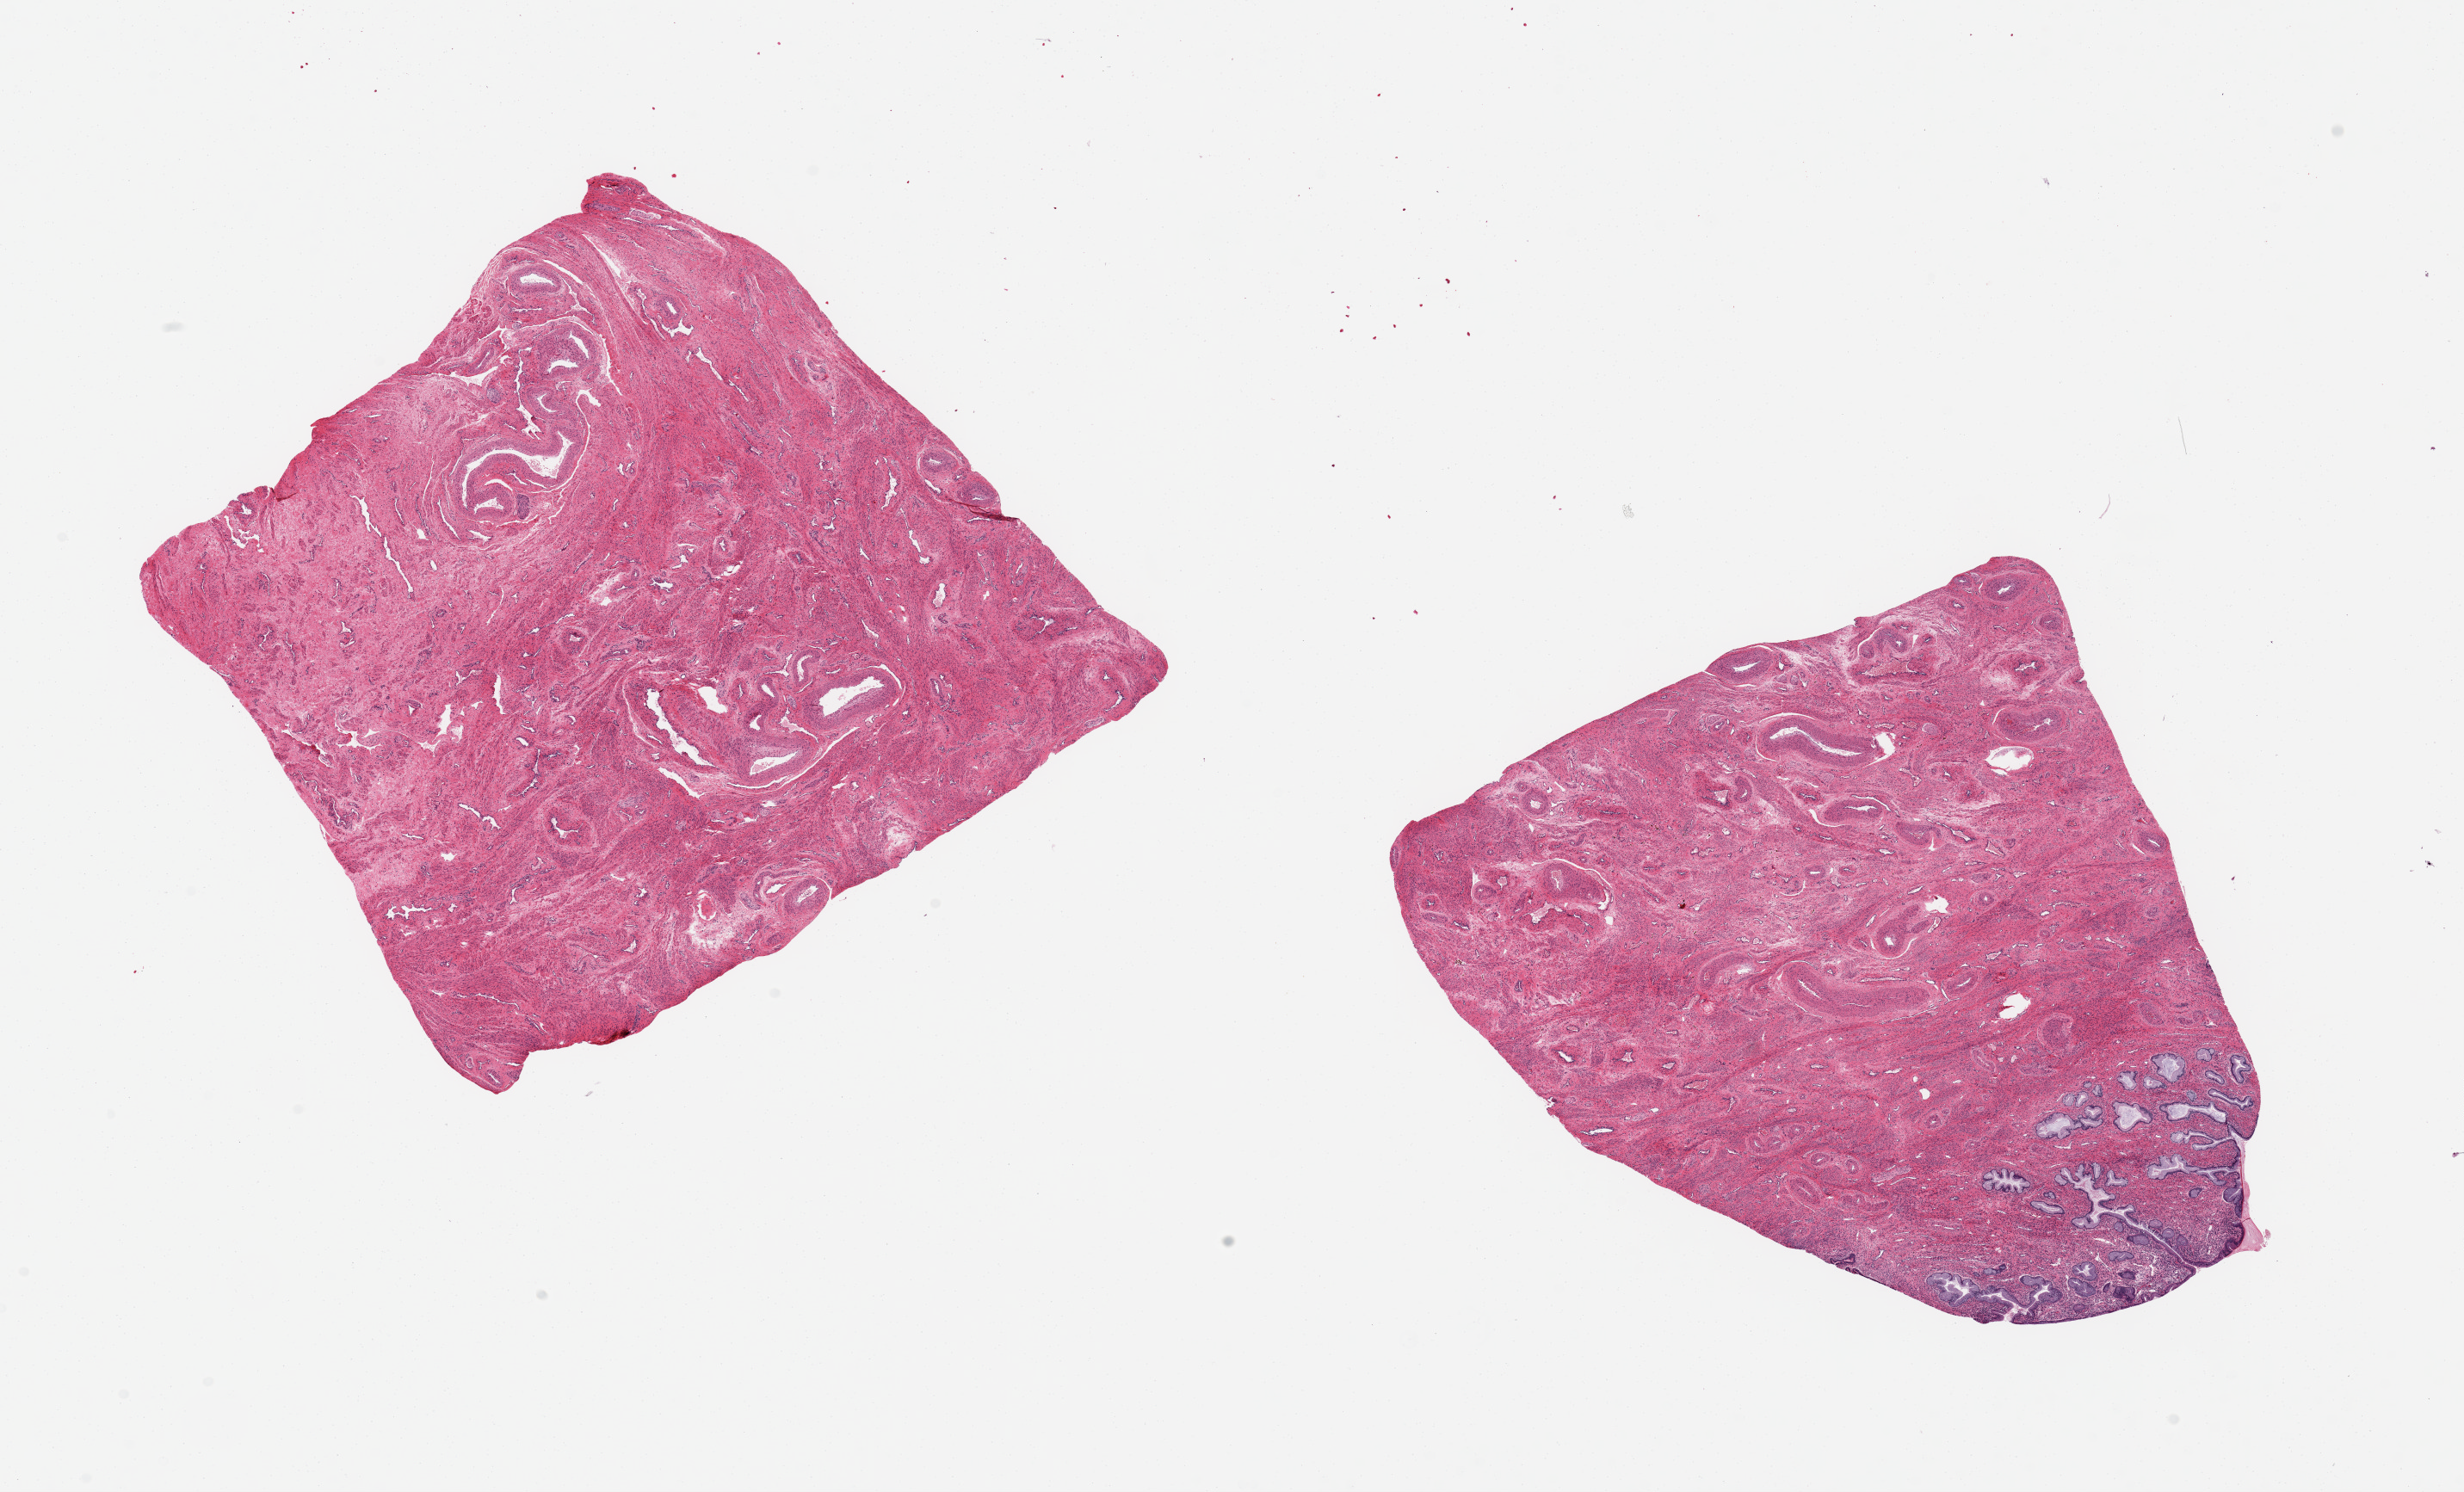
Digitized H&E-stained section, brightfield — low-resolution overview of the scanned area, about 22.6 x 13.7 mm (from a 20x scan); PAXgene-fixed, paraffin-embedded tissue; sampled site (target tissue): endocervix; donor tissue sample. Female donor.
• review note (as recorded): 2 pieces, 7x7 & 7x6 mm; 1 piece is endocervix; other has no epithelium